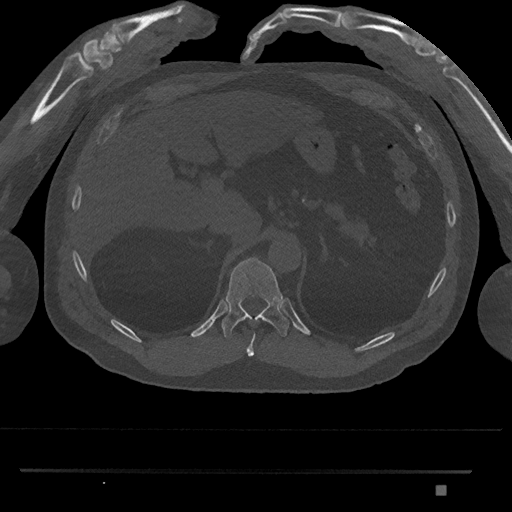
CT including the spine, one axial slice. Position 956 of 1134 along the scan axis. Reconstruction kernel Br40s/3. 120 kVp. Bone window (W 1800 / L 400 HU). 512 × 512 image matrix, field of view 429 × 429 mm. Patient: male, 65 years. From the clinical record (not read from this slice): primary cancer: prostate.
Outlined on this slice (semi-automatically segmented with operator editing):
- T10 vertebra: bounding box [x1, y1, x2, y2] px = [246, 334, 255, 357]
- T11 vertebra: [222, 257, 289, 338]